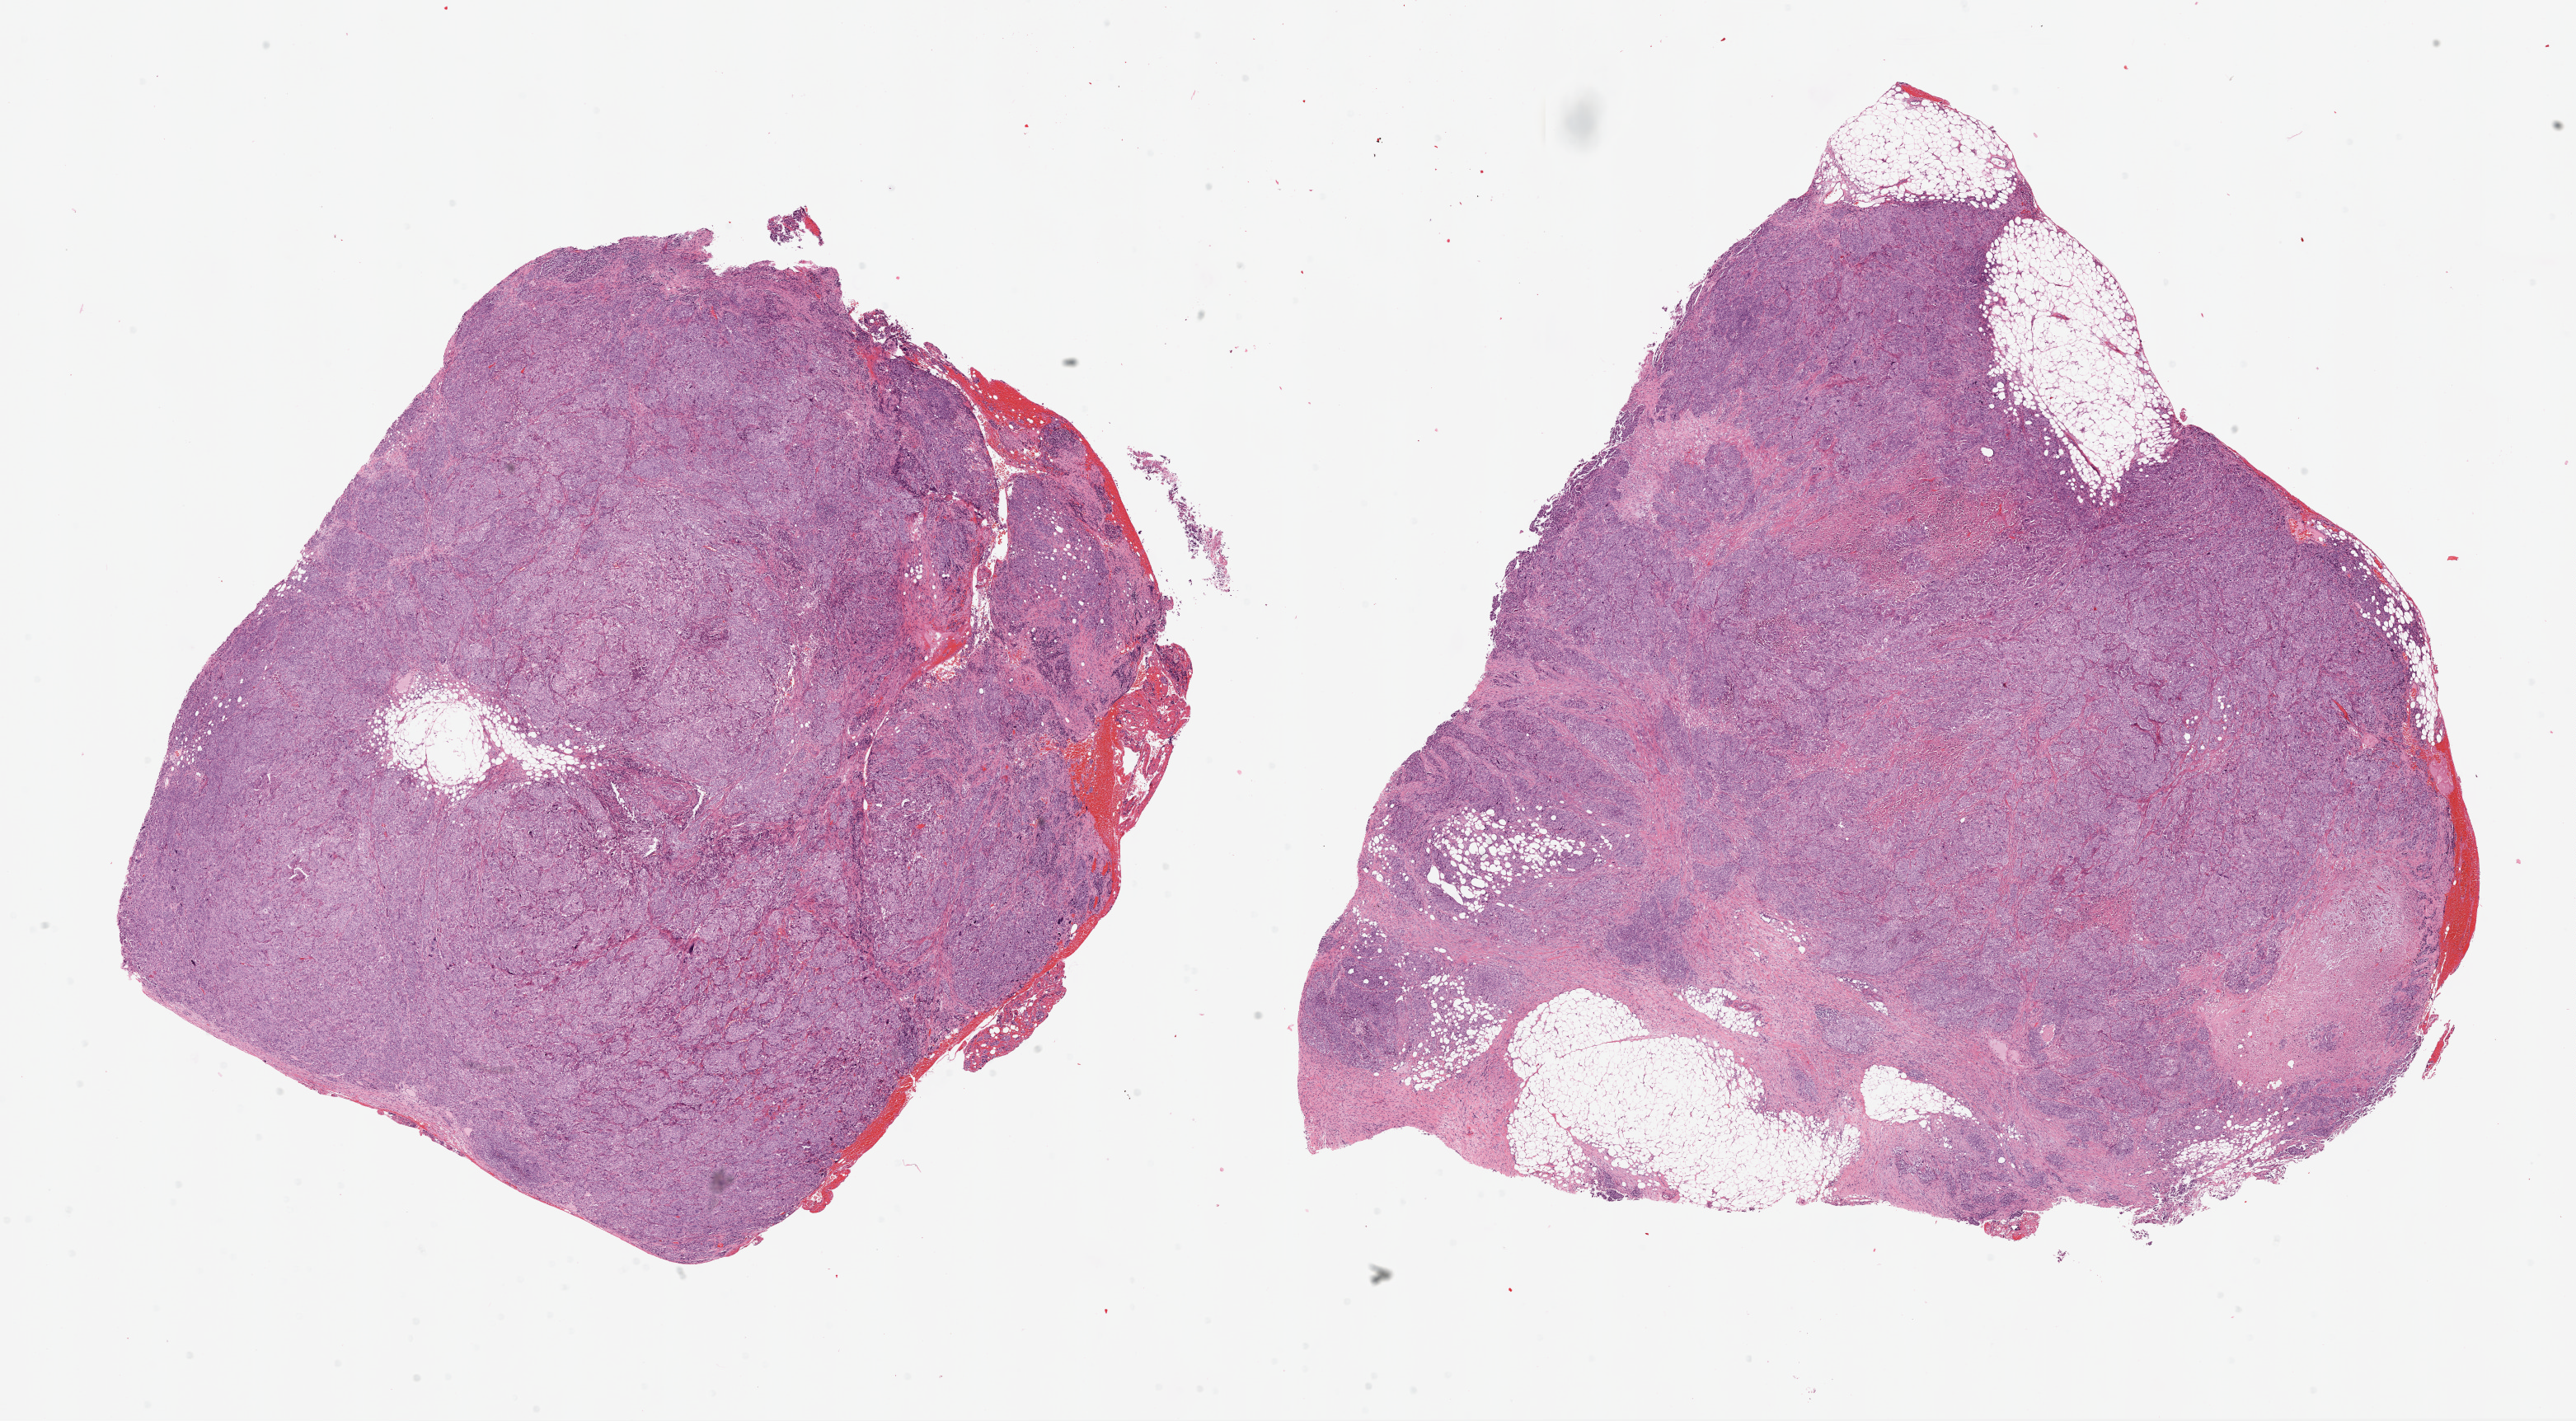
Whole-slide histology image, H&E-stained, shown as a low-resolution overview of the whole scanned area (about 25.1 x 13.8 mm, from a 20x scan). Slide review estimates, as recorded: tumour cells 79%, tumour nuclei 85%, normal cells 8%, stromal cells 10%, necrosis 3%.
Specimen: frozen section from the top of the tissue portion; ovary, primary tumour sample.